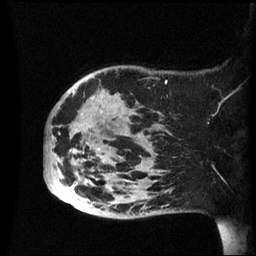
Breast MRI (dynamic contrast-enhanced), one sagittal slice; position 15 of 60 along the scan axis; dynamic contrast-enhanced series, image 2 of 3 at this slice position (ordered by acquisition); 1.5 T; TE 4.2 ms, TR 8.4 ms; 2.4 mm slice thickness; 256 × 256 image matrix, field of view 230 × 230 mm. Female patient, age 49 years.
Outlined on this slice (semi-automatically segmented with operator editing):
- analysis volume of interest (the breast-tissue region the enhancement analysis was run in; not a lesion): bounding box [x1, y1, x2, y2] px = [44, 66, 174, 219]
- tumour enhancement mask (voxels above the 70 % enhancement threshold inside the analysis volume of interest): [74, 91, 137, 216]